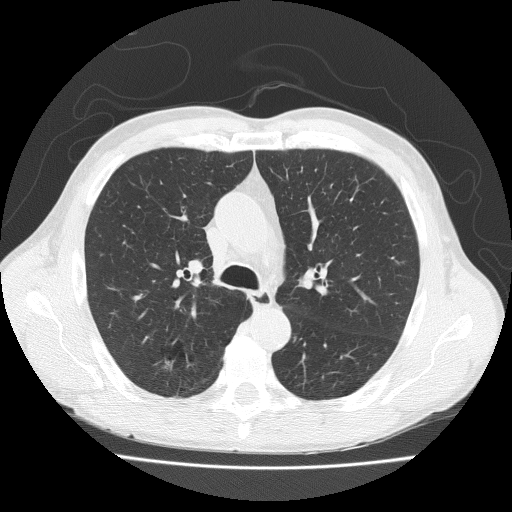
Chest CT (low-dose screening protocol), one axial image. Baseline annual screen. Lung window (W 1500 / L -600 HU). Lung (sharp) reconstruction kernel (FC51). Slice 69 of 203 in the series. Male, age 73 years at enrolment.
Expert-annotated lung lesion, bounding box [x1, y1, x2, y2] px = [145, 338, 197, 386]. Screening reader's record for this exam: no non-calcified nodule ≥4 mm recorded.